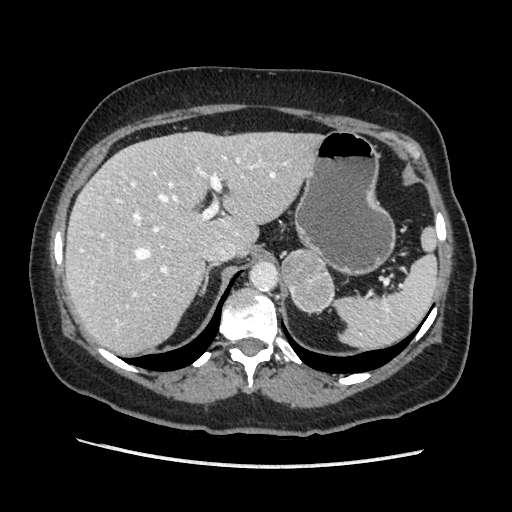
Contrast-enhanced abdominal CT, one axial slice. Slice 139 of 203 in the series (ordered by position). Soft-tissue window (W 400 / L 40 HU). 512 × 512 image matrix, field of view 360 × 360 mm. Female patient. Case-level facts recorded for this patient, not image findings: diagnosis: adrenocortical carcinoma; tumour side: left adrenal; tumour size at pathology: 6.5 cm; Ki-67 index: 22 %; stage (as recorded): 2.
Structures marked on this image (semi-automatic segmentation, software-assisted and operator-edited):
- mass: bounding box (x1, y1, x2, y2) in pixels: (282, 249, 335, 311)